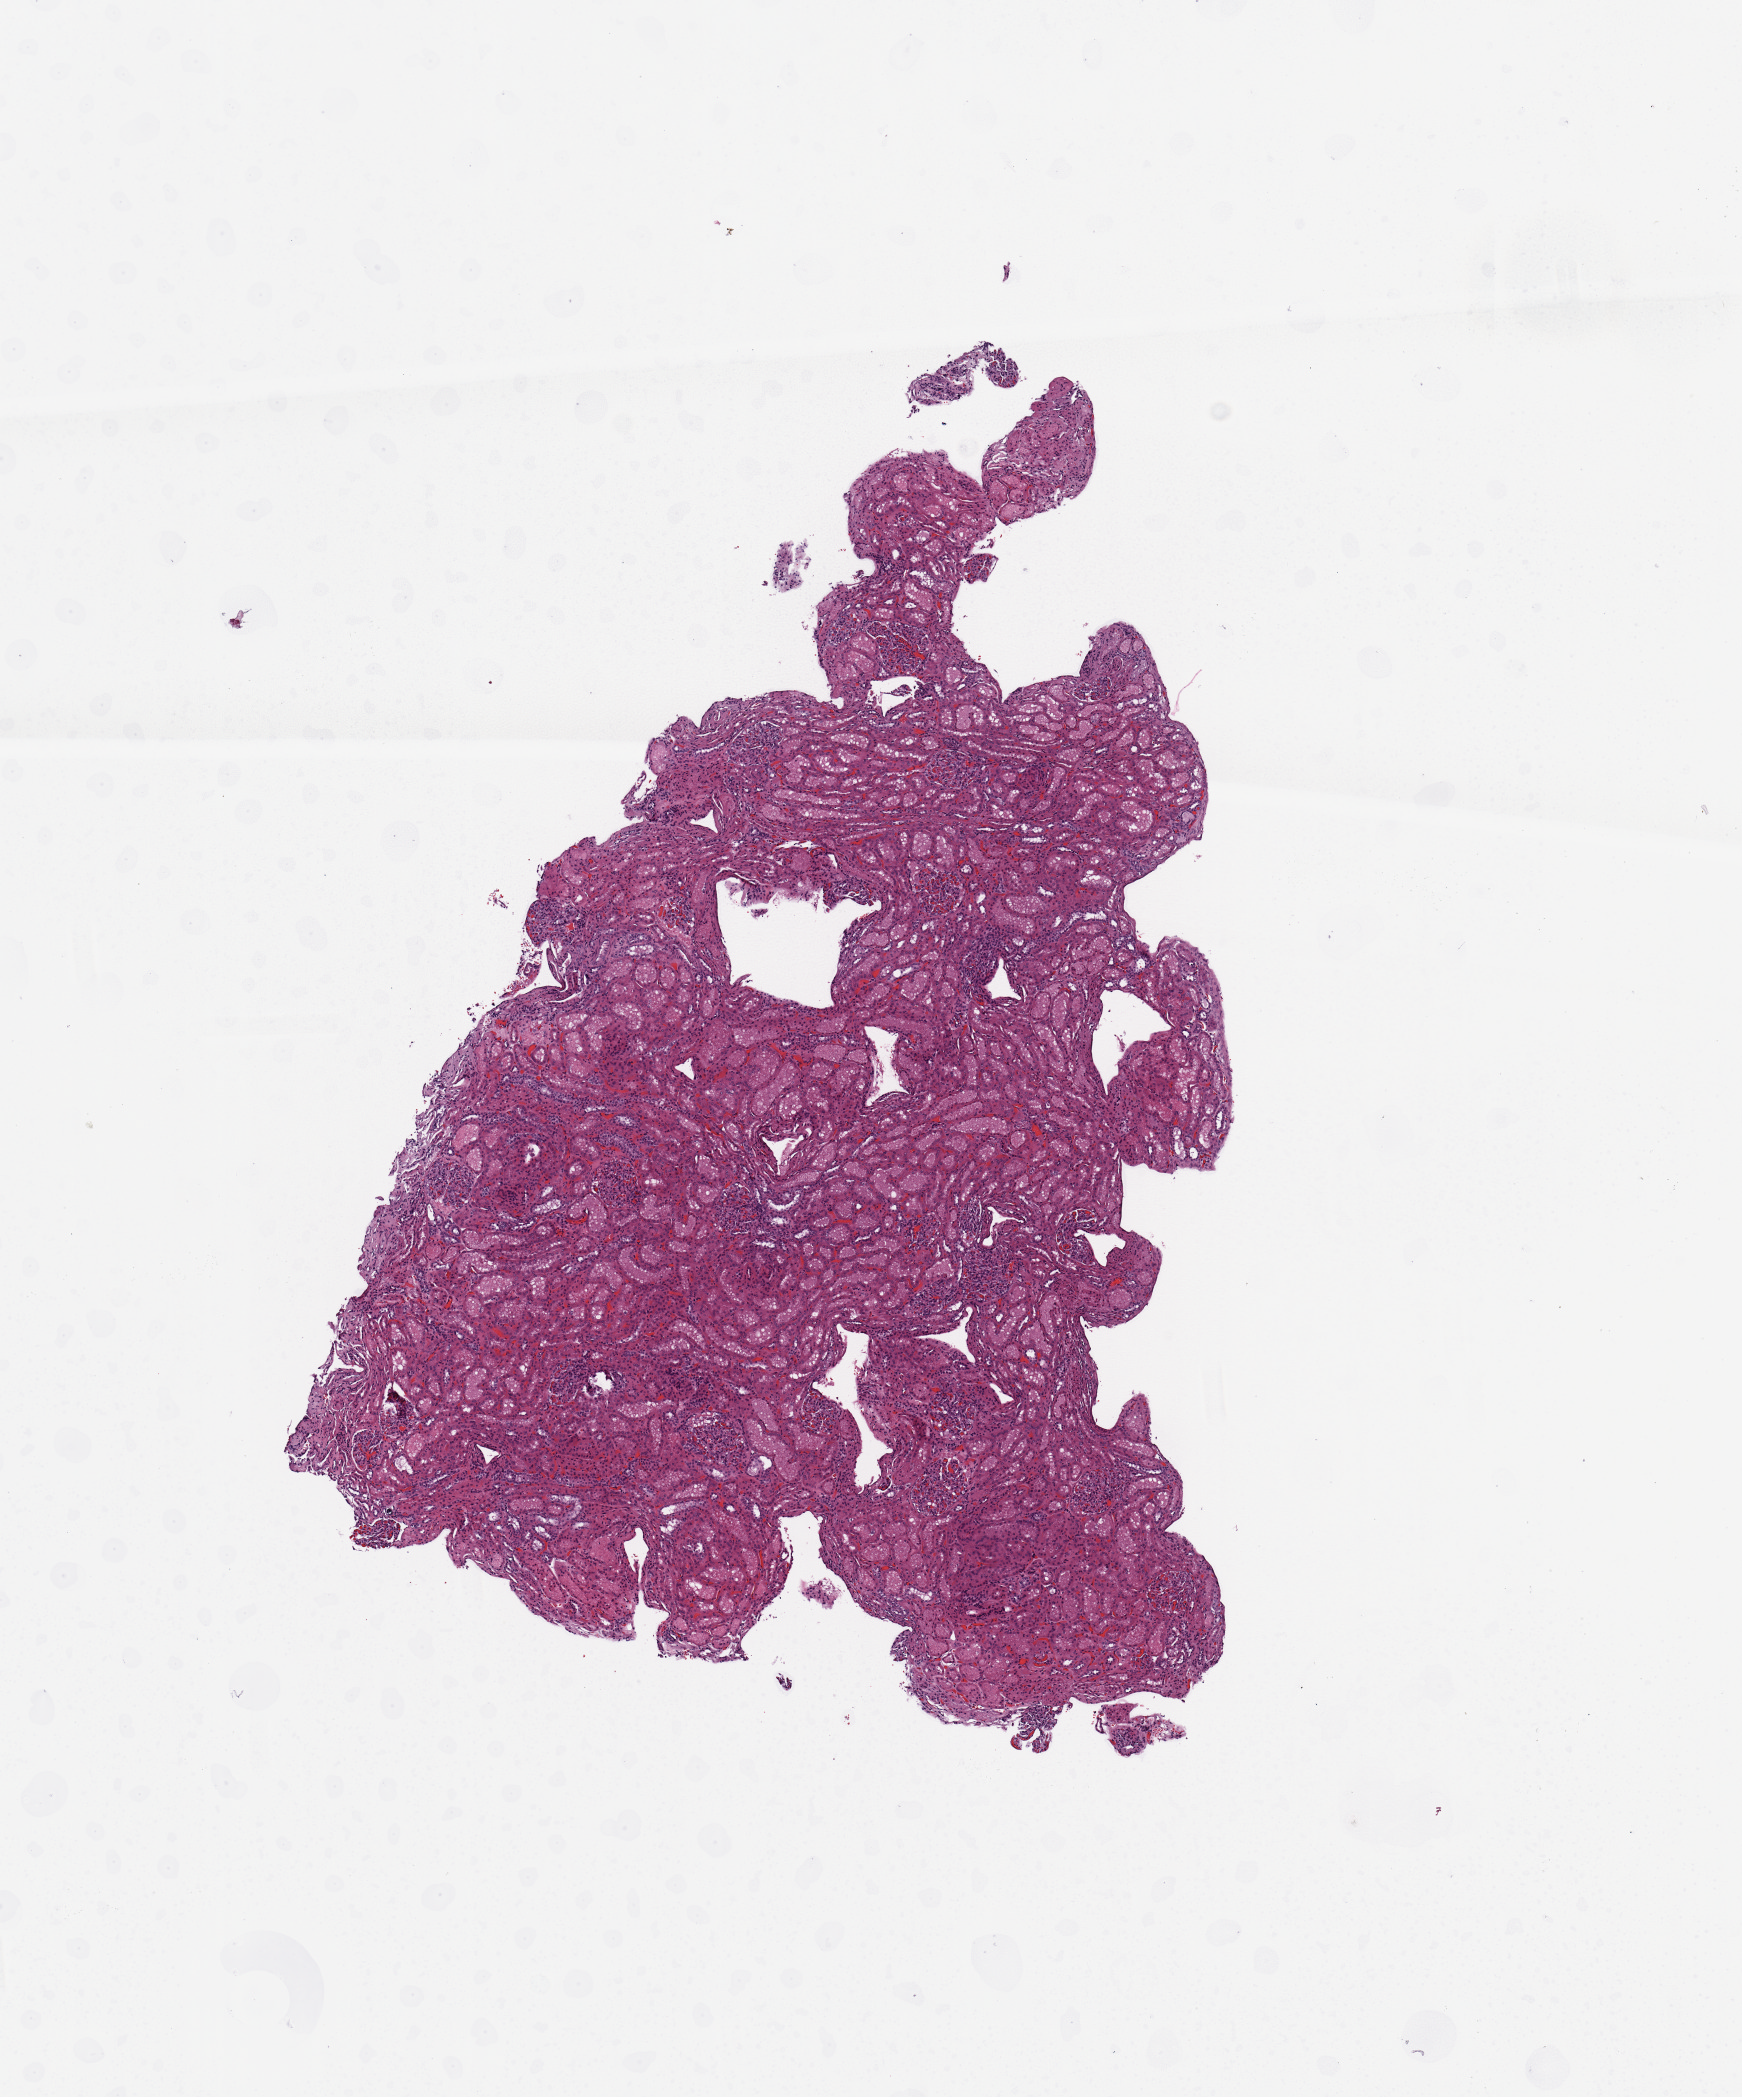
Whole-slide histology image, Hematoxylin and eosin (H&E) stained, shown as a low-resolution overview of the whole scanned area (about 6.9 x 8.3 mm), kidney, normal (non-tumour) tissue. 33-year-old female patient.
This section: normal (non-tumour) tissue from the same patient. Patient diagnosis: Renal cell carcinoma, NOS.